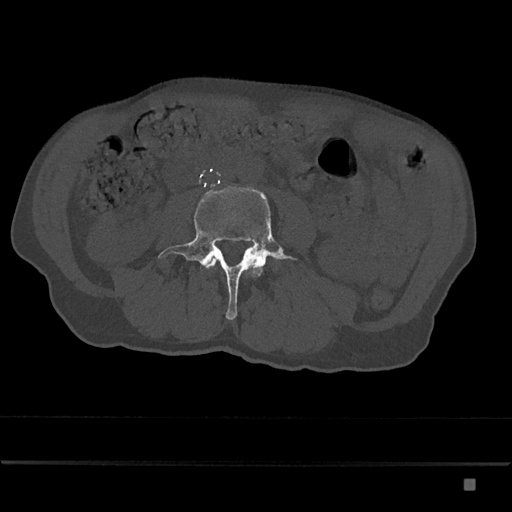
CT including the spine, one axial slice. Position 348 of 797 along the scan axis. 120 kVp. Bone window (W 1800 / L 400 HU). 0.5 mm slice thickness. 512 × 512 image matrix, field of view 390 × 390 mm. Patient: male, 72 years. From the clinical record (not read from this slice): primary cancer: prostate.
Structures marked on this image (semi-automatic segmentation, software-assisted and operator-edited):
- L3 vertebra: bounding box <207,258,254,269> (left, top, right, bottom; pixels)
- L4 vertebra: <158,186,297,320>